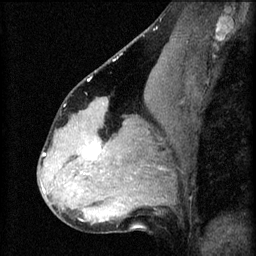
Breast MRI (dynamic contrast-enhanced), one sagittal slice. Slice 35 of 60 in the series (ordered by position). 3 images stored at this slice position (order not interpretable as contrast timing). 1.5 T. TE 4.2 ms, TR 8.2 ms. 256 × 256 image matrix, field of view 180 × 180 mm. Patient: female, 37 years.
Annotated regions visible in this slice (semi-automatic segmentation, software-assisted and operator-edited):
- analysis volume of interest (the breast-tissue region the enhancement analysis was run in; not a lesion): bounding box <67,120,122,179> (left, top, right, bottom; pixels)
- tumour enhancement mask (voxels above the 70 % enhancement threshold inside the analysis volume of interest): <86,144,102,159>